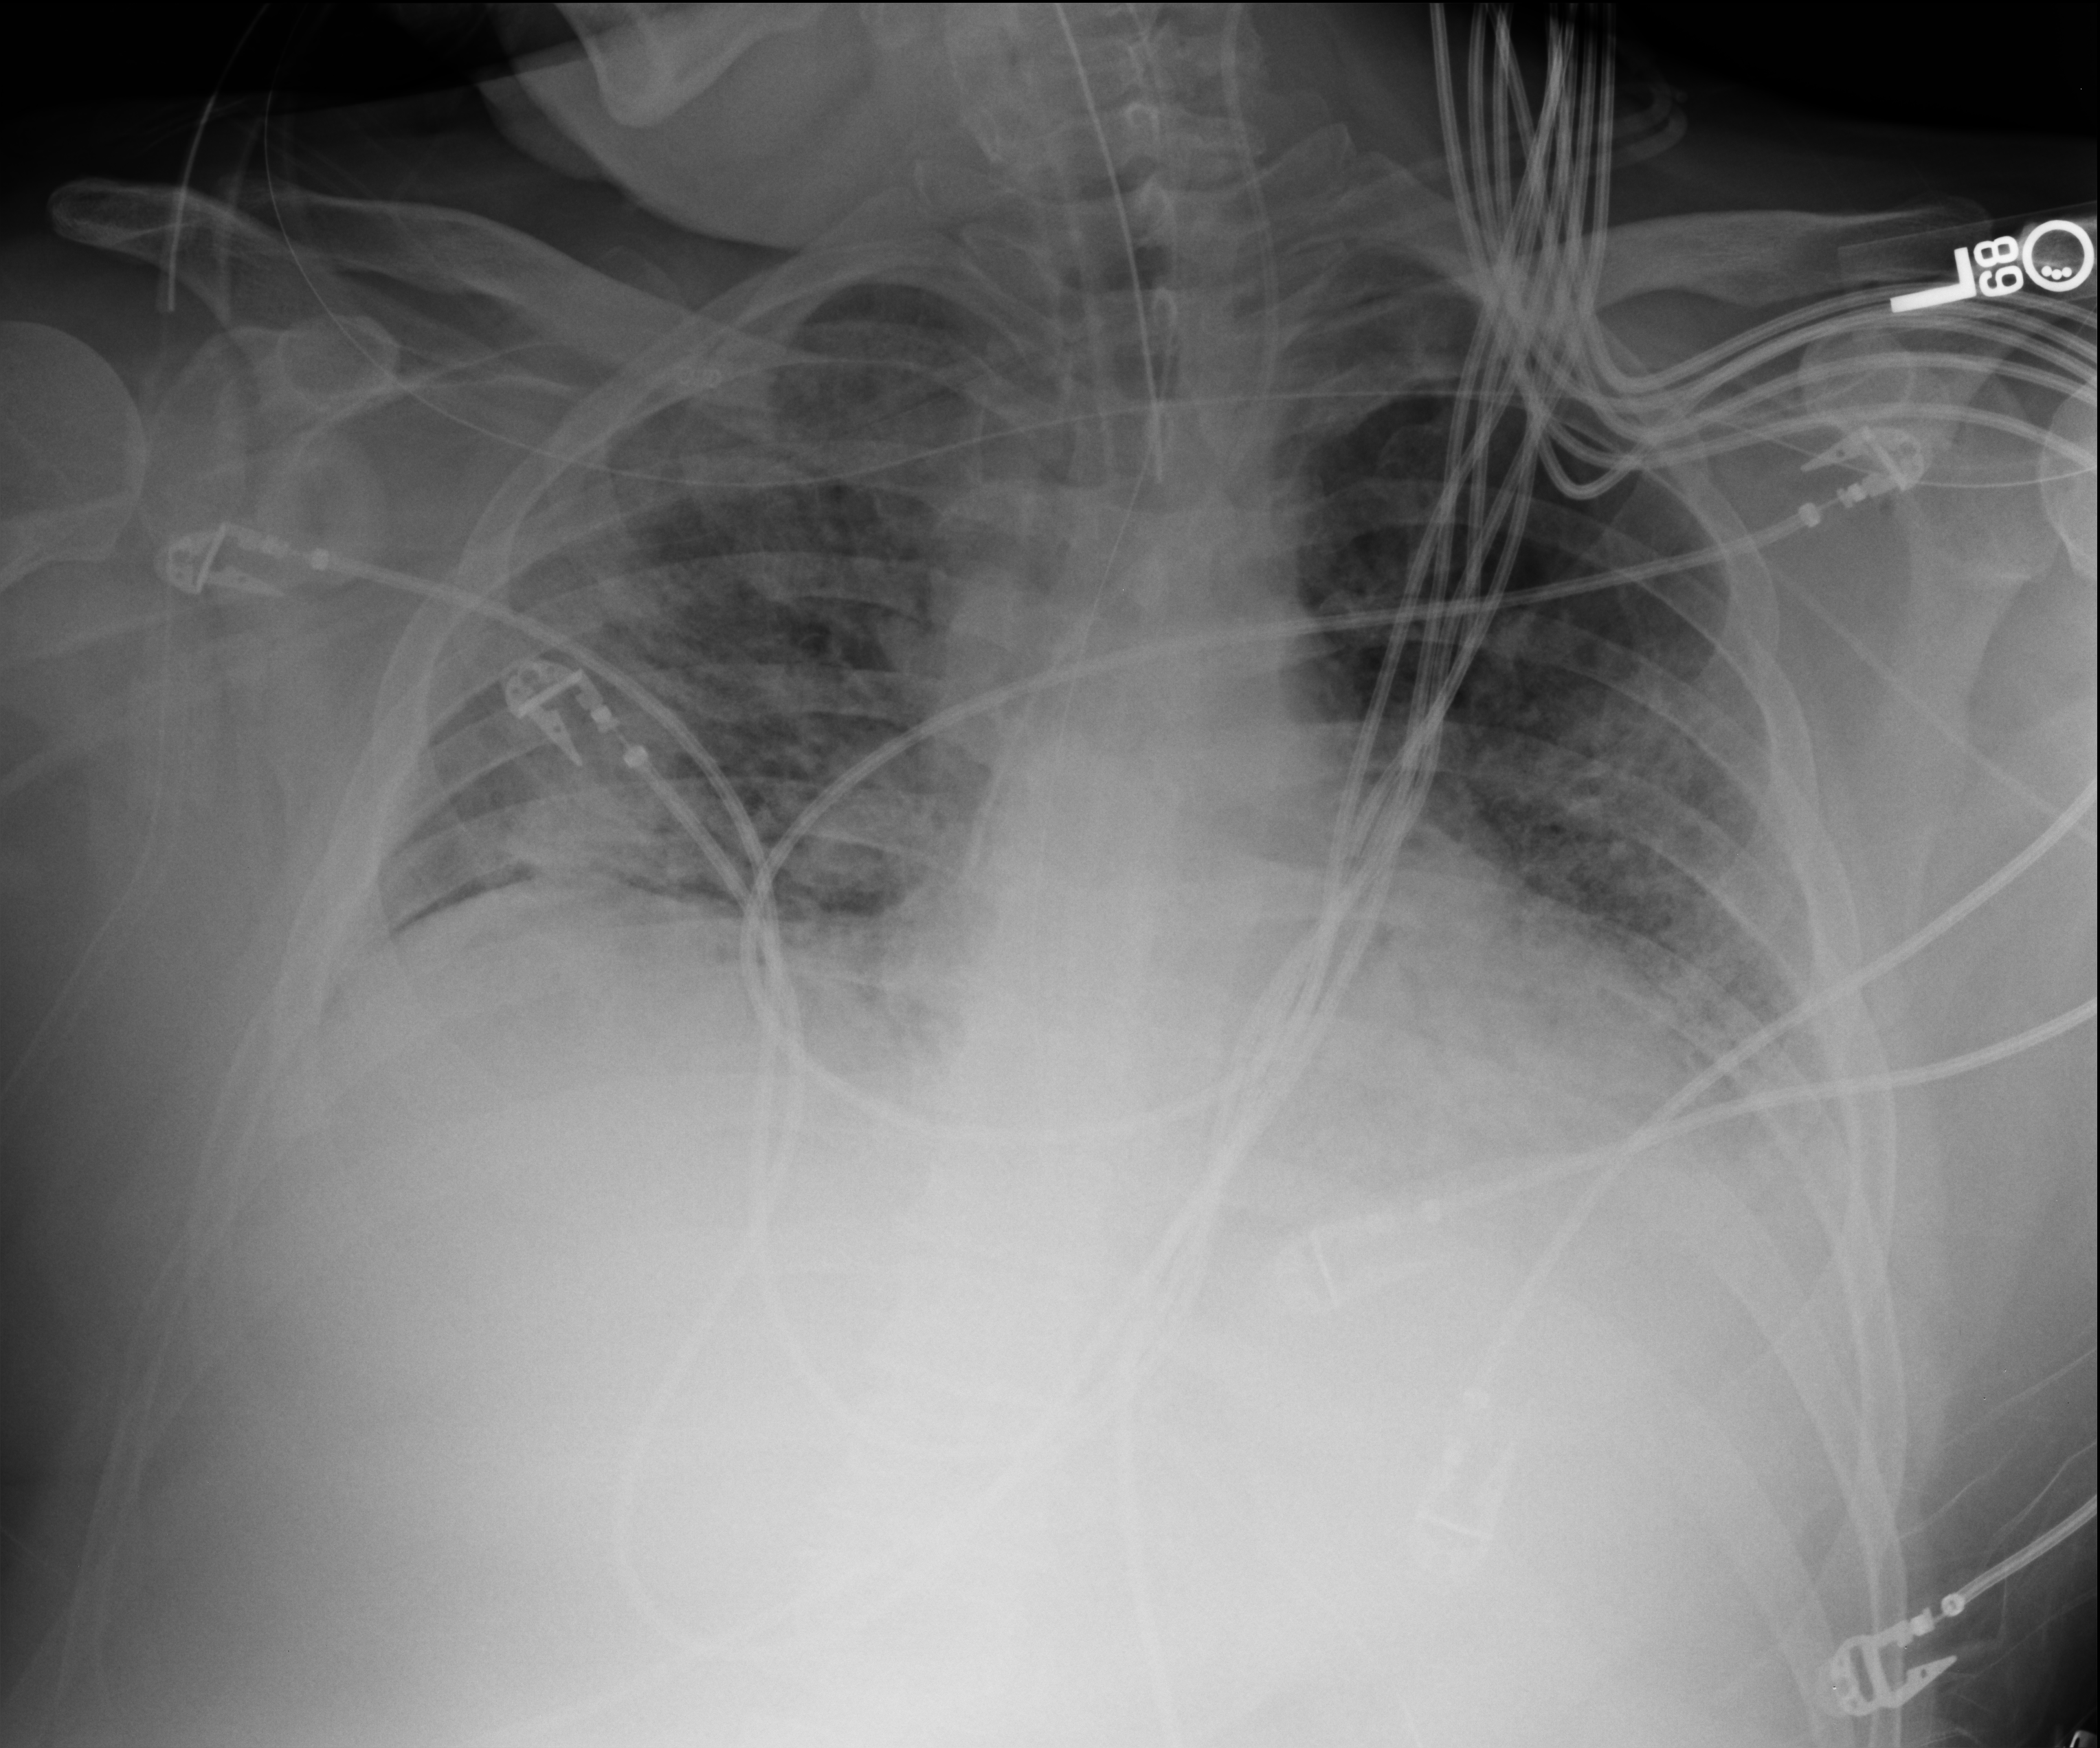
Chest X-ray (portable); anteroposterior (AP) projection. Patient hospitalised with COVID-19; male, aged 18–59 years.
Hospital-stay facts (about this admission, not read from this image; timing relative to this image not recorded):
- length of hospital stay: 80 days
- COPD (admission record): no